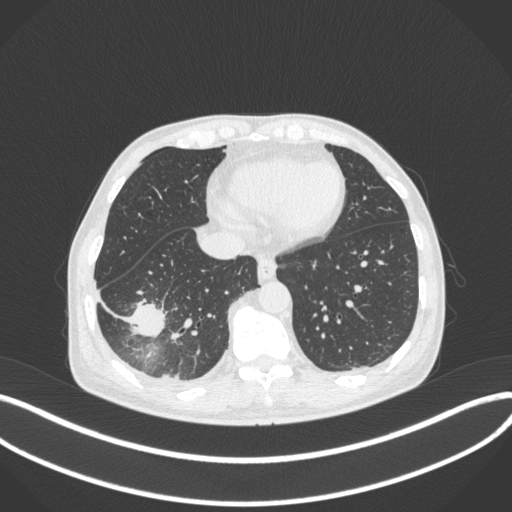
Chest CT, one axial slice. Position 105 of 385 along the scan axis. Reconstruction kernel B31f. 120 kVp. Lung window (W 1500 / L -600 HU). 512 × 512 image matrix, field of view 400 × 400 mm. Male patient, age 64 years. From the clinical record (not read from this slice): clinical TNM (as recorded): T3 N0 M0.
Outlined on this slice (bounding box drawn by a radiologist):
- lung tumour (recorded histology: adenocarcinoma): bounding box <129,292,169,343> (left, top, right, bottom; pixels)